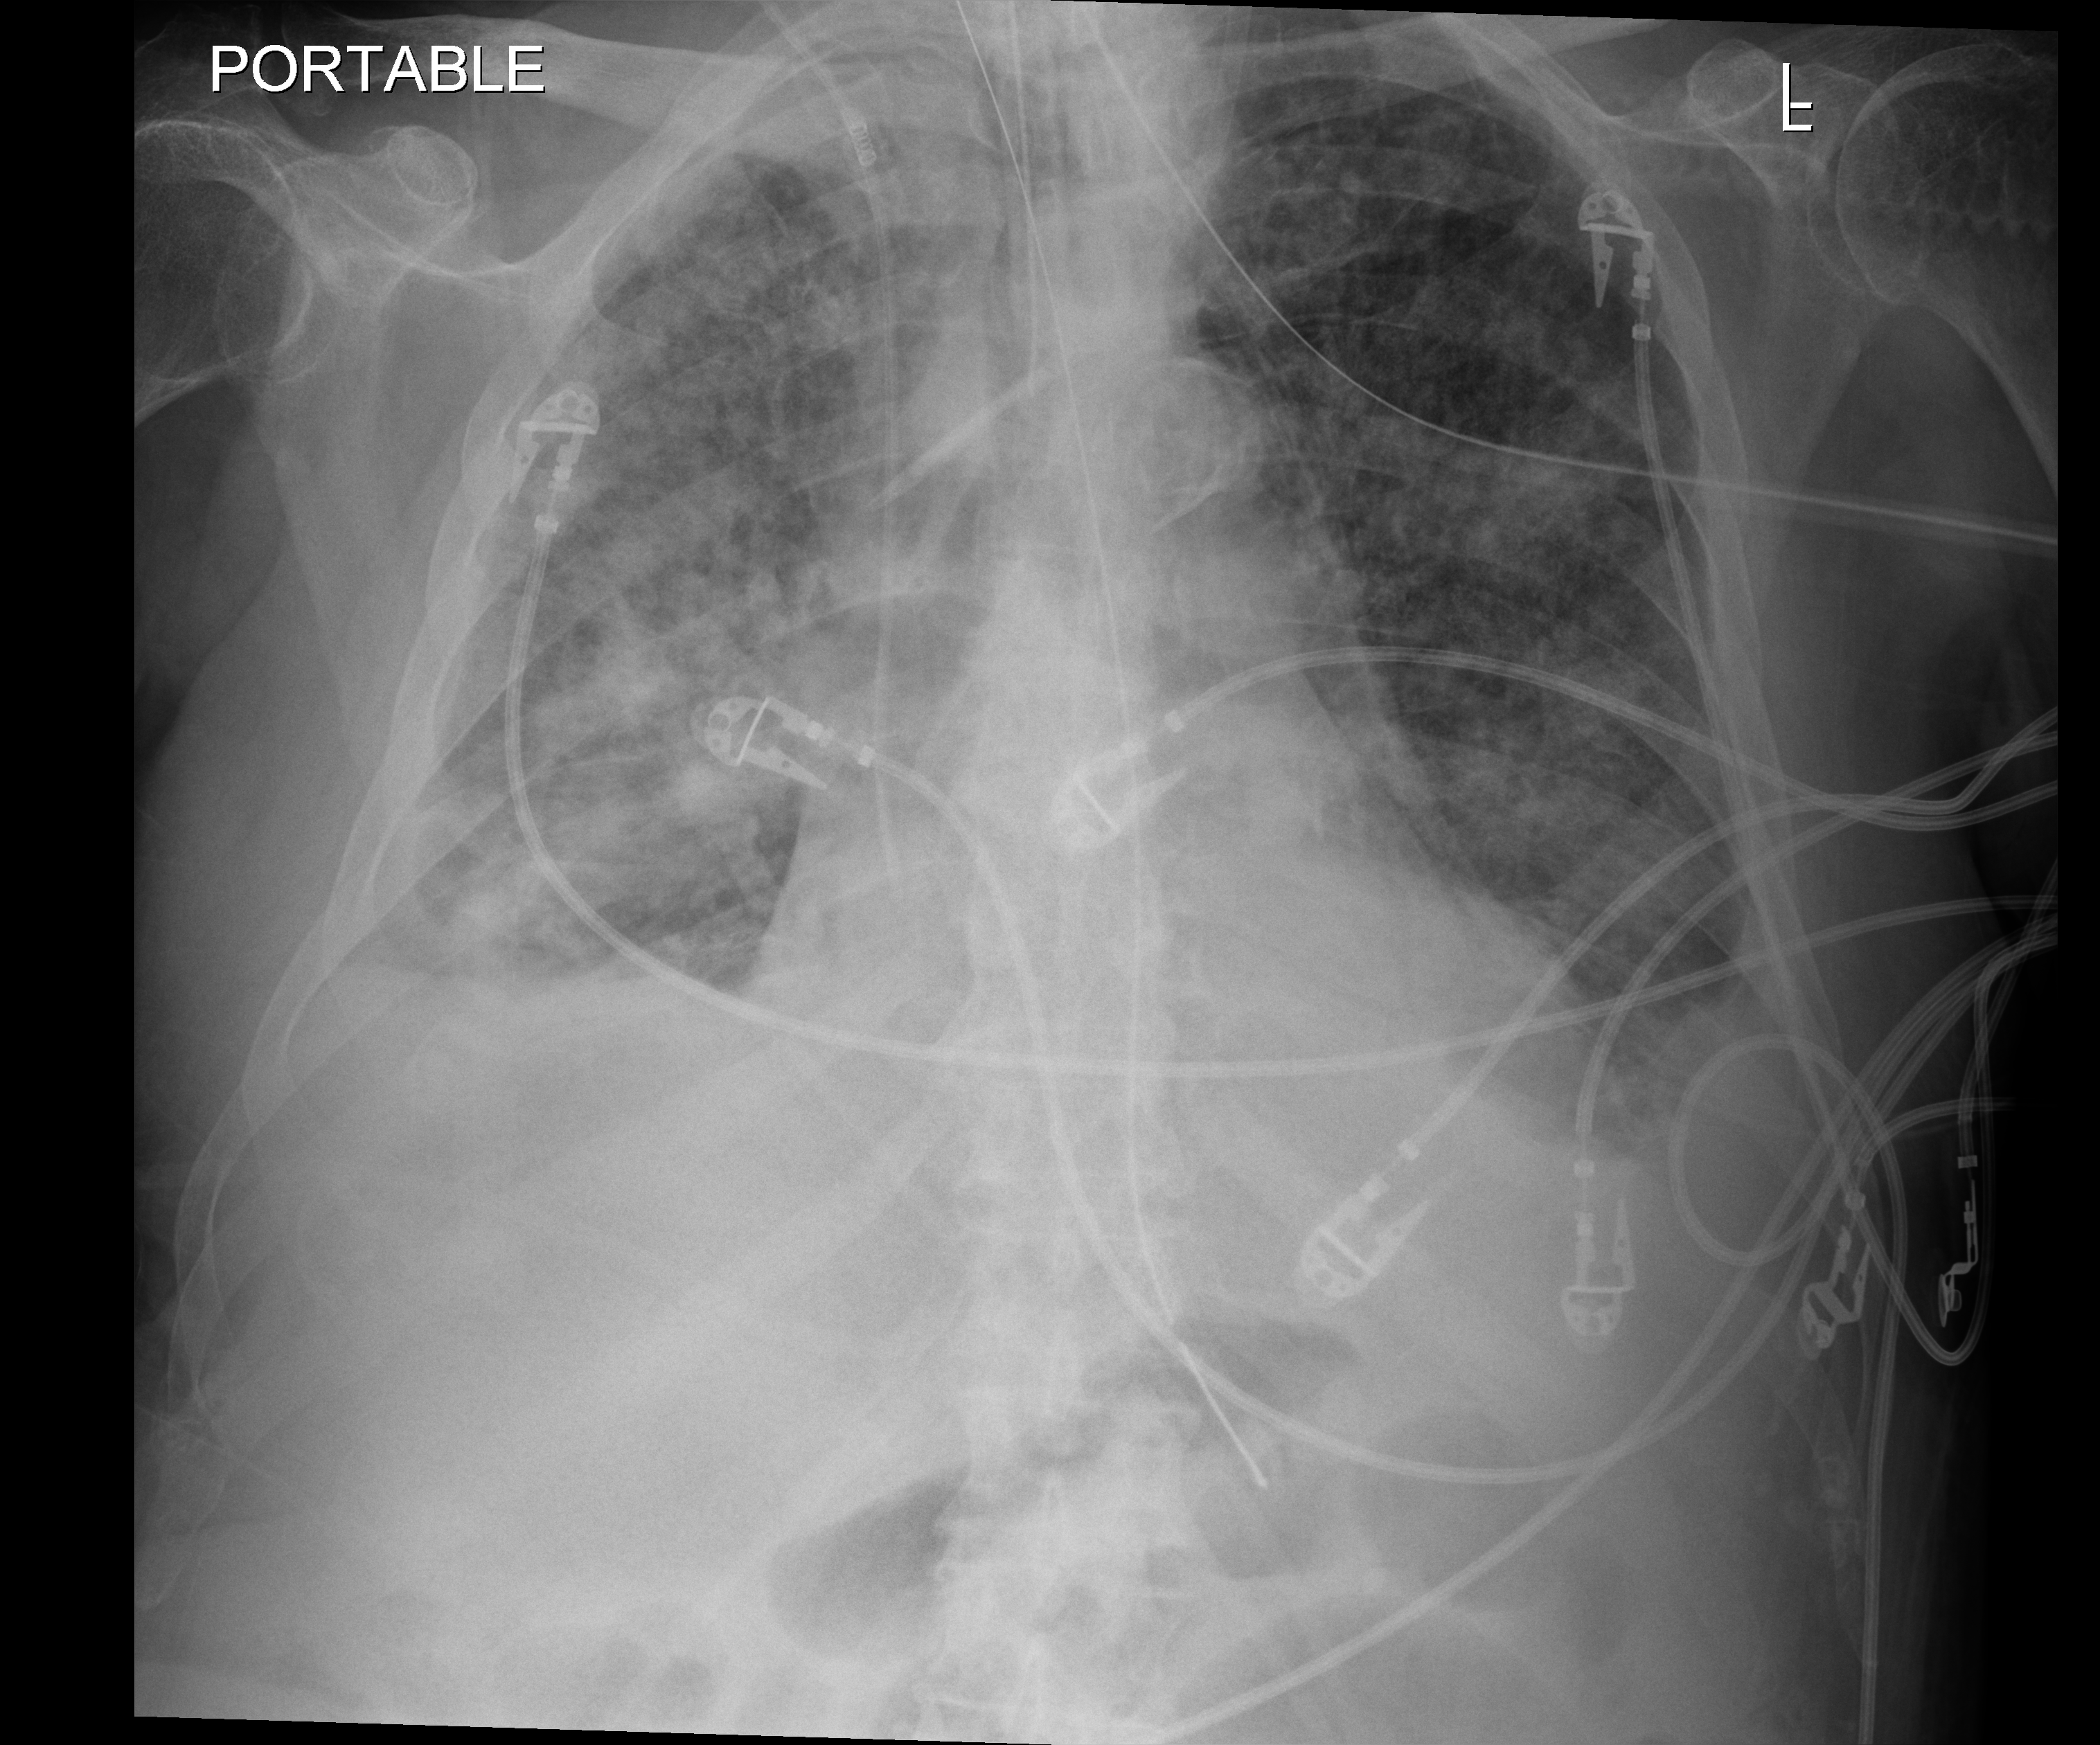
Chest X-ray (portable); anteroposterior (AP) projection. Male patient hospitalised with COVID-19, age 75–90 years.
From the hospital-stay record, not from the radiograph (when in the stay this image was taken is not recorded): length of hospital stay: 28 days; mechanically ventilated during this hospital stay: yes; admitted to intensive care during this hospital stay: yes.